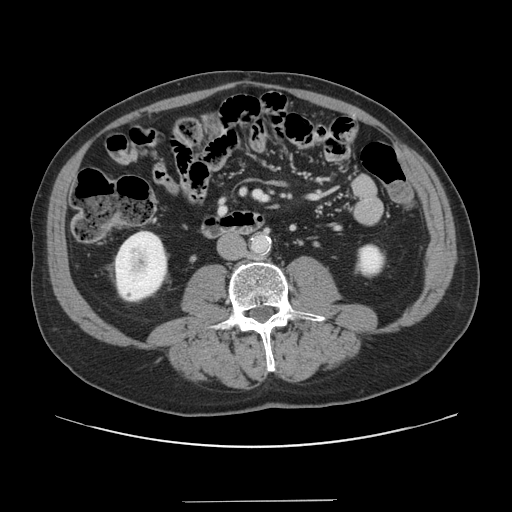
Contrast-enhanced abdominal CT, one axial slice. Slice 26 of 151 in the series (ordered by position). 120 kVp. Intravenous contrast given. Soft-tissue window (W 400 / L 40 HU). 512 × 512 image matrix, field of view 399 × 399 mm. Male patient, age 63 years. From the clinical record (not read from this slice): diagnosis: colorectal cancer liver metastases, imaged before liver resection; multiple liver metastases: no; largest metastasis: 2.1 cm; chemotherapy before resection: no.
Structures marked on this image (expert manual segmentation):
- portal vein (with intrahepatic branches): bounding box [x1, y1, x2, y2] px = [254, 191, 266, 200]